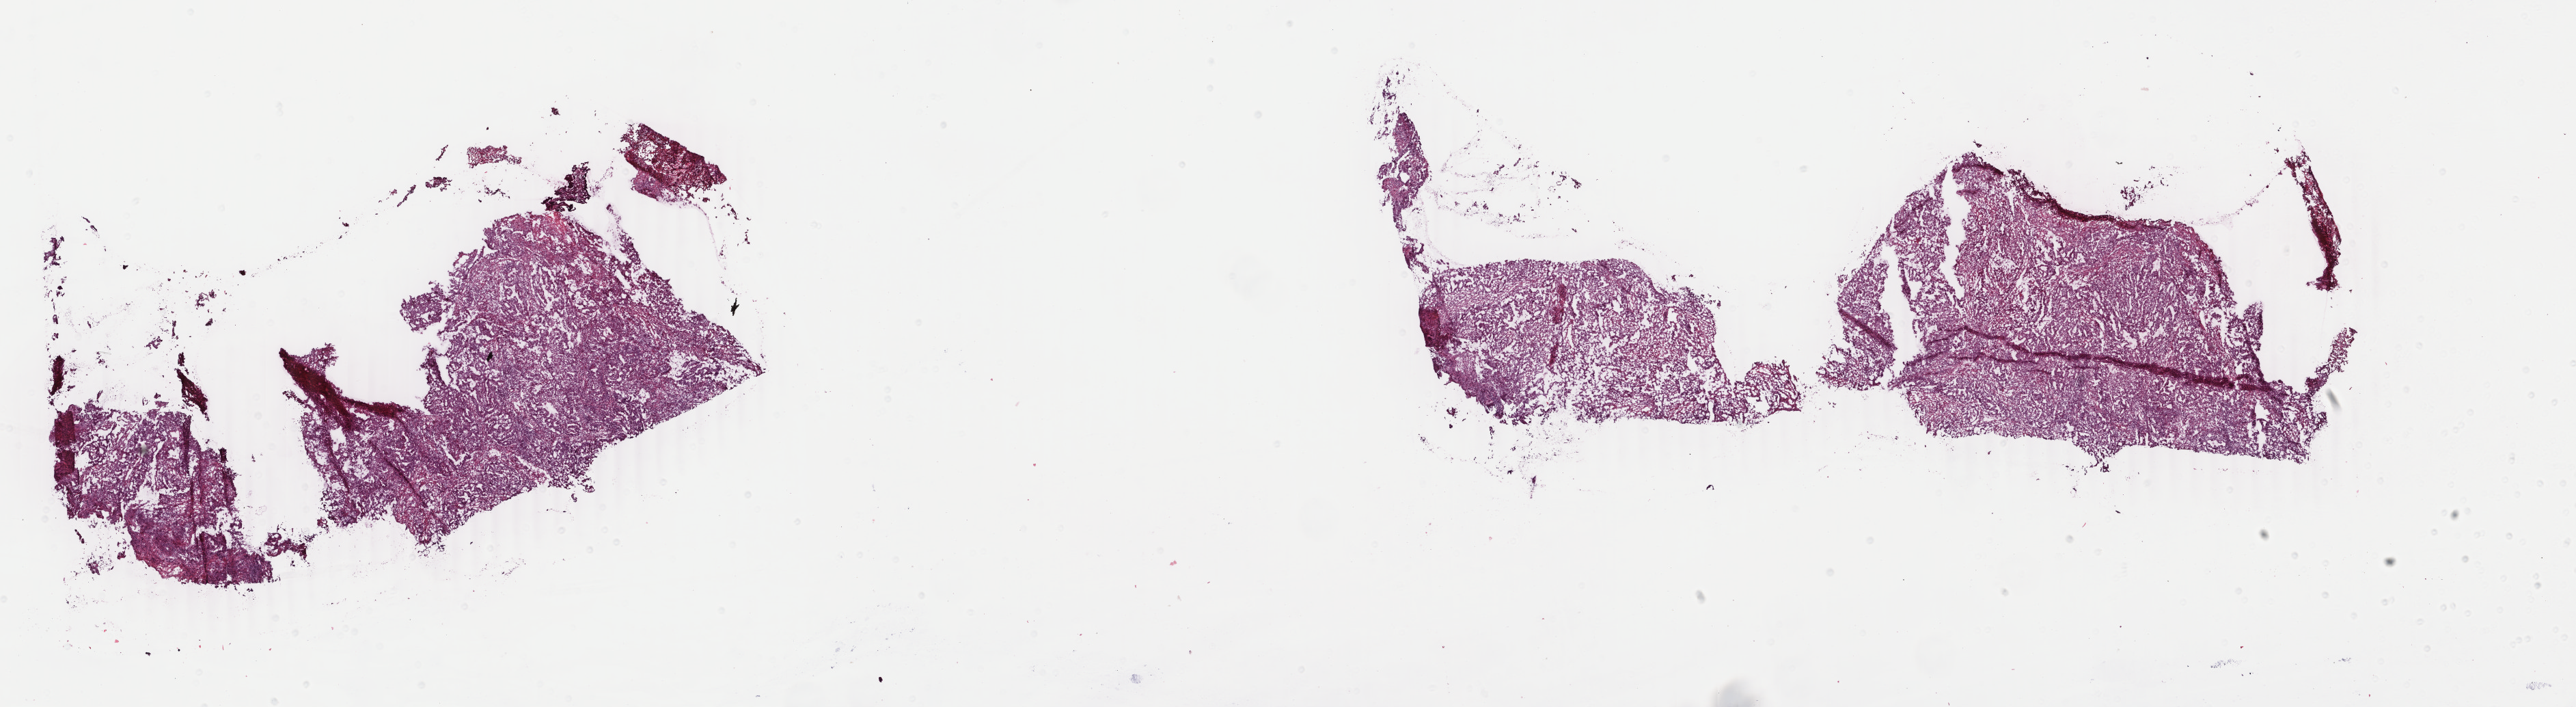
Digitized H&E-stained tissue section (whole slide), low-resolution overview of the scanned area, about 30.0 x 8.2 mm (acquisition: 40x scan). Frozen section from the top of the tissue portion. Primary tumour sample from the uterus. Female patient; age at initial diagnosis 53 years. Histologic grade: G3 (poorly differentiated). Slide review estimates, as recorded: tumour cells 57%, tumour nuclei 60%, normal cells 0%, stromal cells 40%, necrosis 3%. Inflammatory infiltration, as recorded: lymphocyte infiltration 4%, monocyte infiltration 0%, neutrophil infiltration 0%.
* pathologic diagnosis: Endometrioid adenocarcinoma, NOS
* FIGO stage: IB